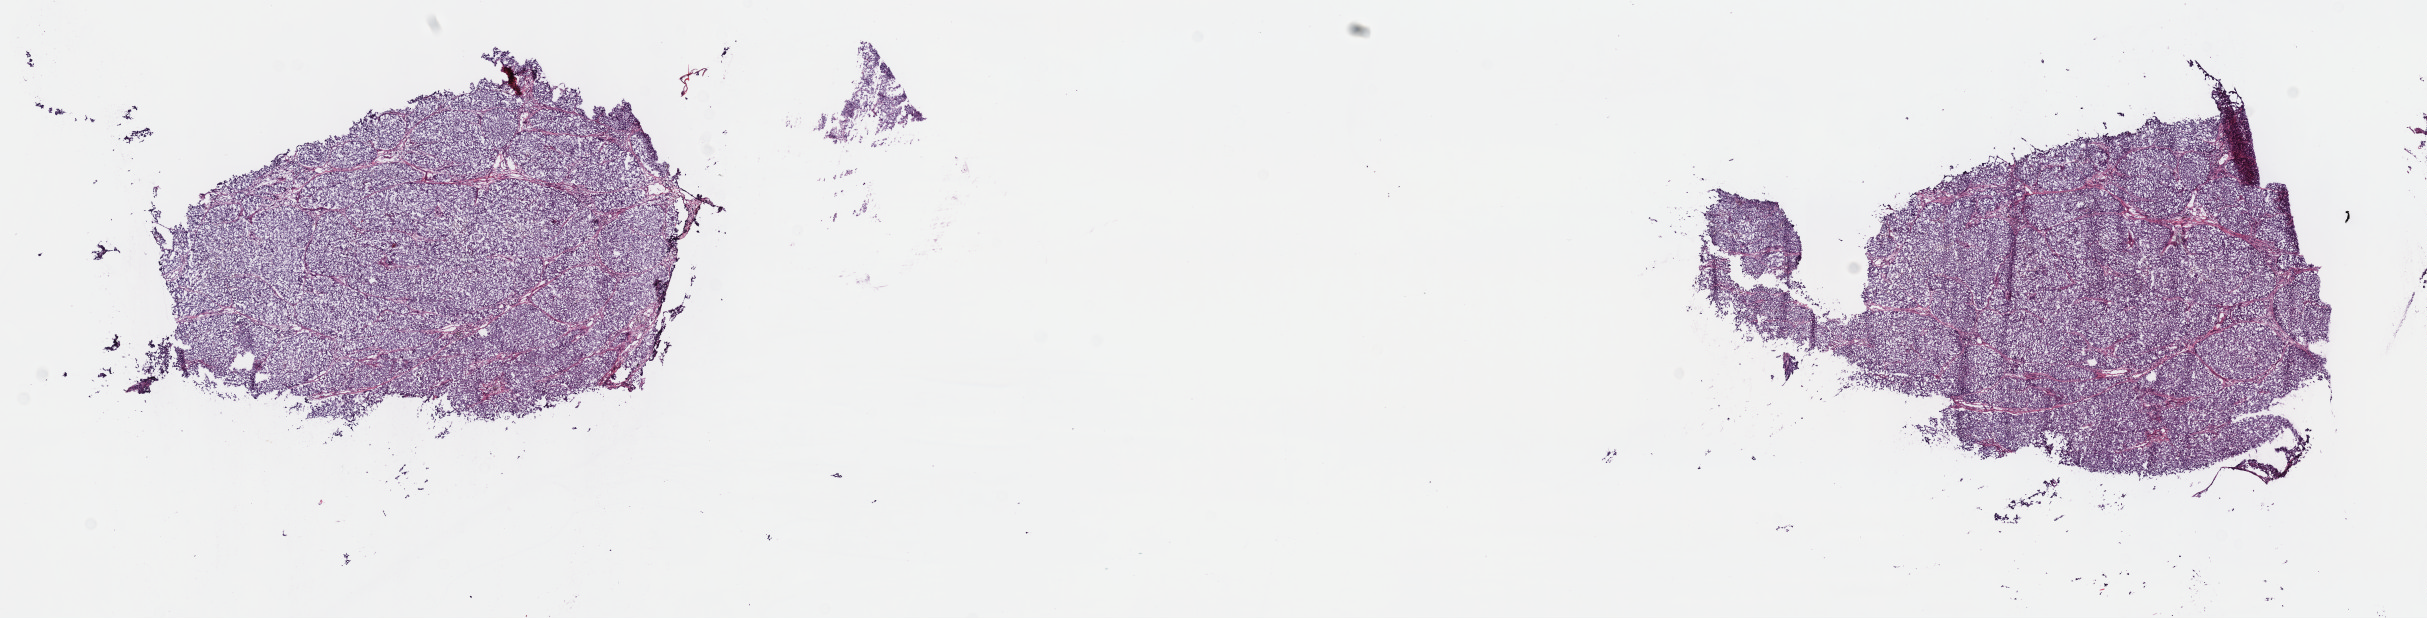
Digitized Hematoxylin and eosin (H&E) stained tissue section (whole slide), whole scanned area (about 19.6 x 5.0 mm, acquisition: 40x scan) shown as a low-resolution overview. Frozen section from the top of the tissue portion. Sample: primary tumour, skin. Male patient; age at initial diagnosis 77 years. Slide review estimates, as recorded: tumour cells 100%, tumour nuclei 80%, normal cells 0%, stromal cells 0%, necrosis 0%. Infiltration values recorded for this section: lymphocyte infiltration 2%, monocyte infiltration 0%, neutrophil infiltration 0%.
* AJCC pathologic stage: IIC (7th edition)
* histologic diagnosis: Mixed epithelioid and spindle cell melanoma